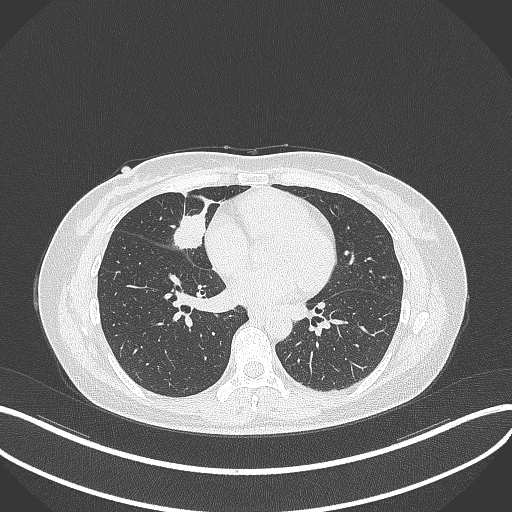
Chest CT, one axial slice; reconstruction kernel B70f; 120 kVp; lung window (W 1500 / L -600 HU); 1 mm slice thickness; 512 × 512 image matrix, field of view 400 × 400 mm. Patient: female, 43 years. Case-level facts recorded for this patient, not image findings: clinical TNM (as recorded): T1c N3 M1; histopathological grade: G1.
Annotated regions visible in this slice (bounding box drawn by a radiologist):
- lung tumour (recorded histology: adenocarcinoma): box from (x=170, y=204) to (x=209, y=259) px